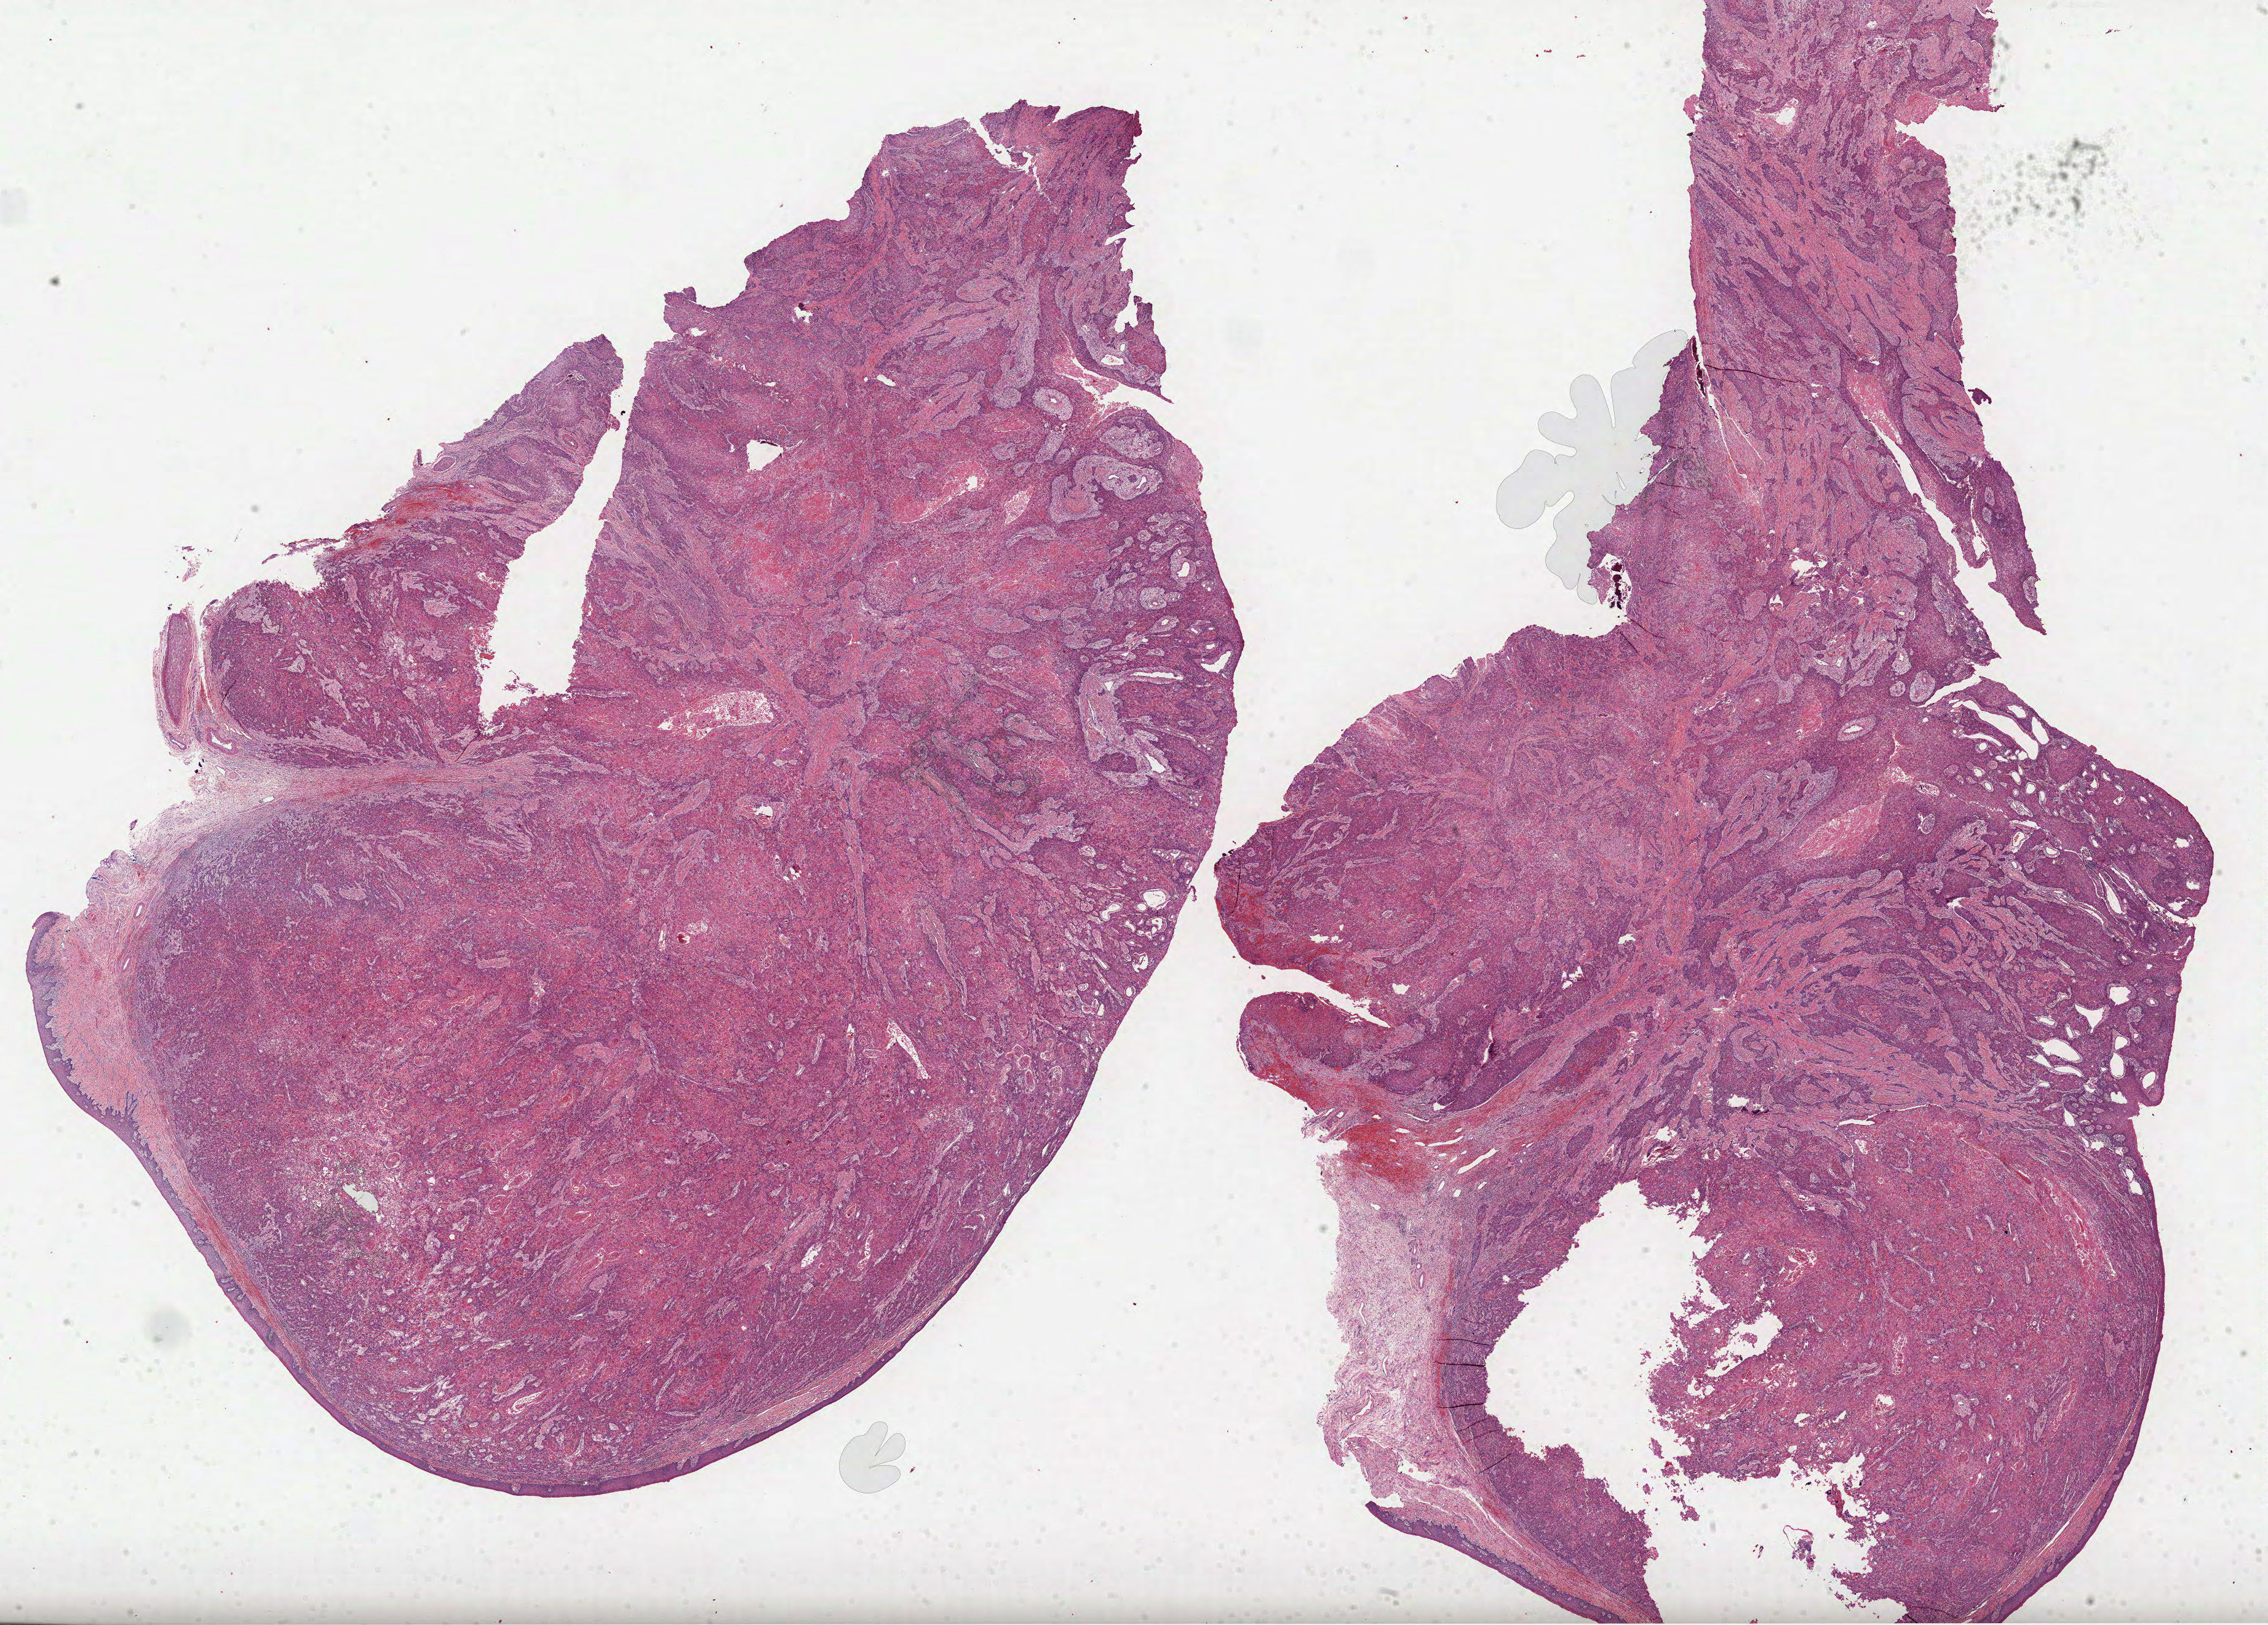
Whole-slide histology image, H&E-stained — a low-resolution overview of the entire scanned area, about 29.7 x 21.3 mm; formalin-fixed paraffin-embedded (FFPE) diagnostic section; head and neck, primary tumour sample. Female patient; age at initial diagnosis 60 years. Histologic grade: G2 (moderately differentiated).
• TNM: T4a N2b M0
• AJCC pathologic stage: IVA (6th edition)
• histologic diagnosis: Squamous cell carcinoma, NOS